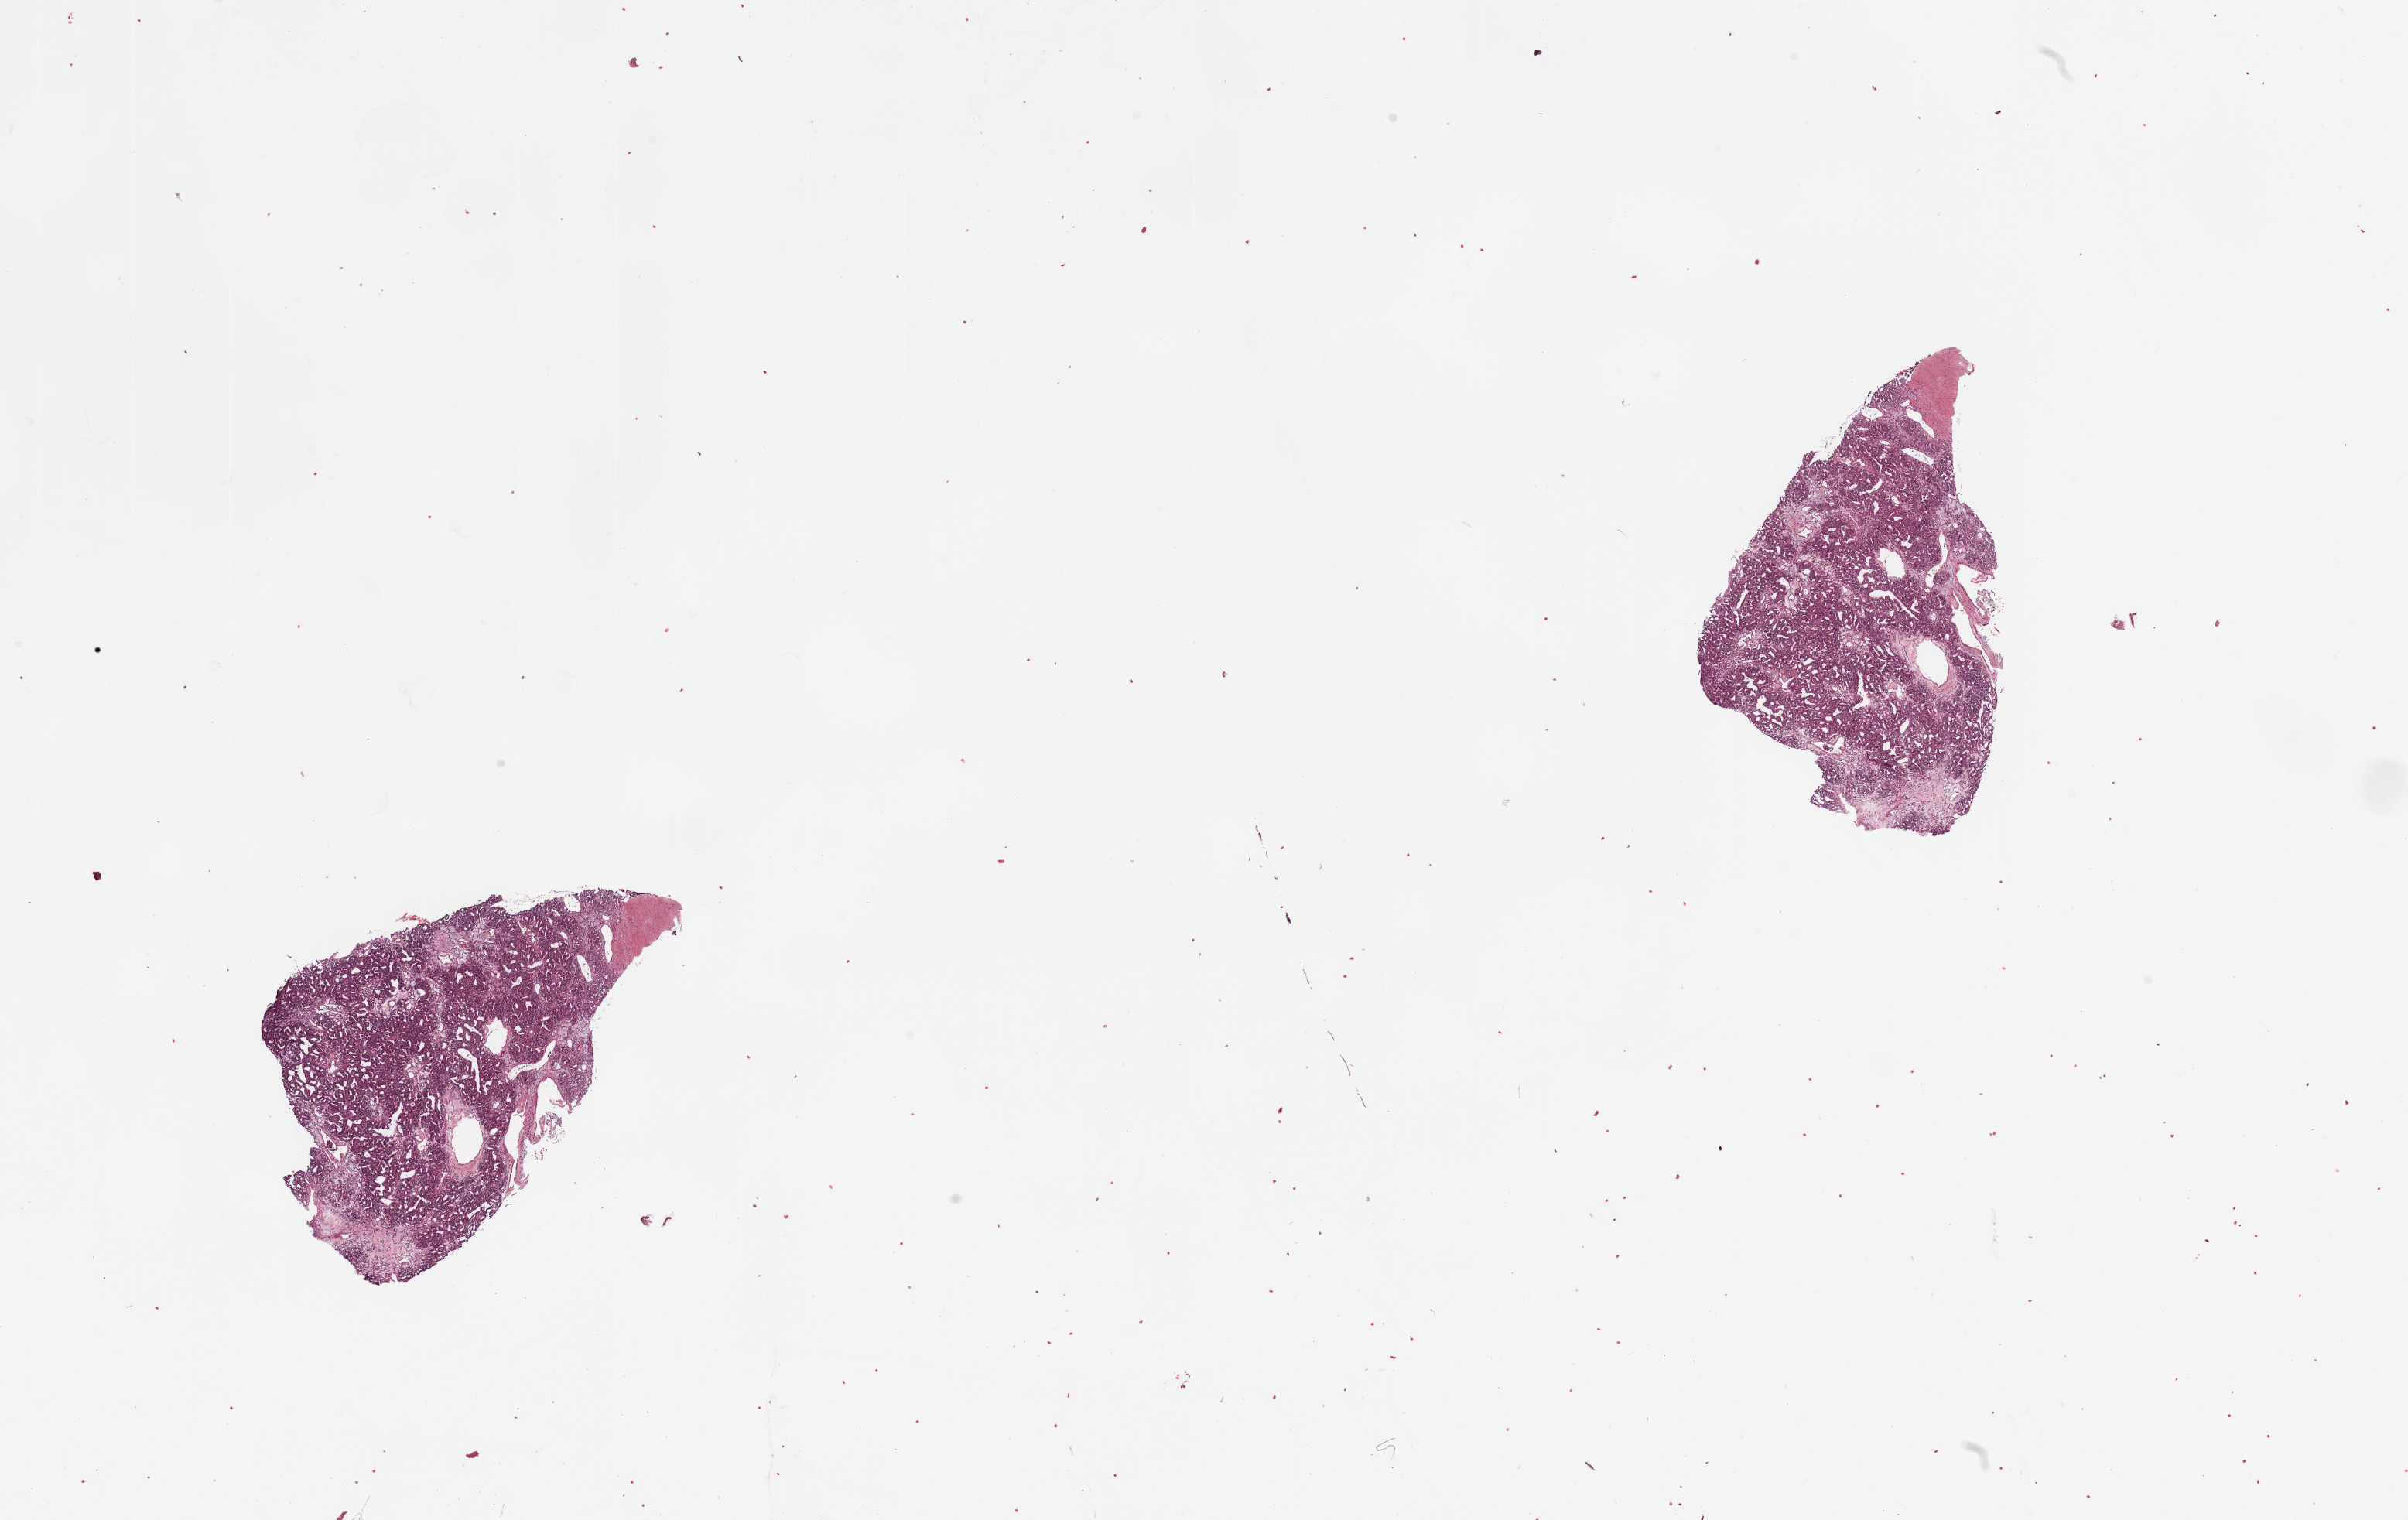
Whole-slide histology image, Hematoxylin and eosin (H&E) stained, whole scanned area (about 24.6 x 15.5 mm) shown as a low-resolution overview, tumour tissue sample, kidney. Patient: male, age 51 years. Histologic grade: G2 (moderately differentiated).
- primary tumour site (as recorded): upper pole
- AJCC pathologic stage: III
- diagnosis: Renal cell carcinoma, NOS